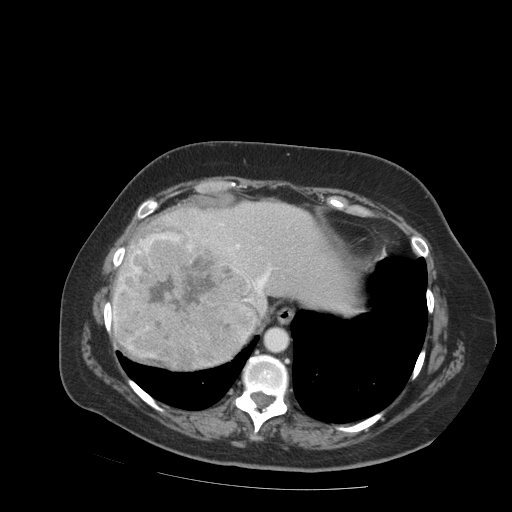
Contrast-enhanced abdominal CT (liver protocol), one axial slice; position 73 of 99 along the scan axis; reconstruction kernel STANDARD; 140 kVp; soft-tissue window (W 400 / L 40 HU); 512 × 512 image matrix. From the clinical record (not read from this slice): diagnosis: hepatocellular carcinoma (patient treated with transarterial chemoembolisation; whether this scan precedes or follows treatment is not stated here); TNM stage (as recorded): Stage-IVB; Child-Pugh class: A; tumour differentiation: moderately differentiated.
Outlined on this slice (semi-automatic segmentation, software-assisted and operator-edited):
- abdominal aorta: bounding box (x1, y1, x2, y2) in pixels: (265, 328, 287, 351)
- liver parenchyma outside the tumour (the mass and vessels are separate outlines, so this box may not span the whole liver): (112, 200, 352, 370)
- mass: (110, 229, 266, 371)
- liver vessels: (219, 223, 270, 288)